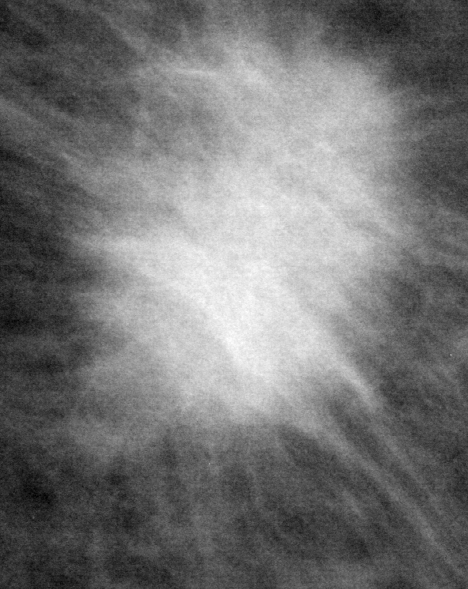
Cropped region of a digitized screen-film mammogram centred on a radiologist-marked abnormality; left breast; MLO view.
Marked abnormality: mass, shape irregular, margins spiculated; BI-RADS assessment category 5; subtlety rating 5 on a 1 (subtle) to 5 (obvious) scale; pathology result (as recorded, not read from the image): malignant.